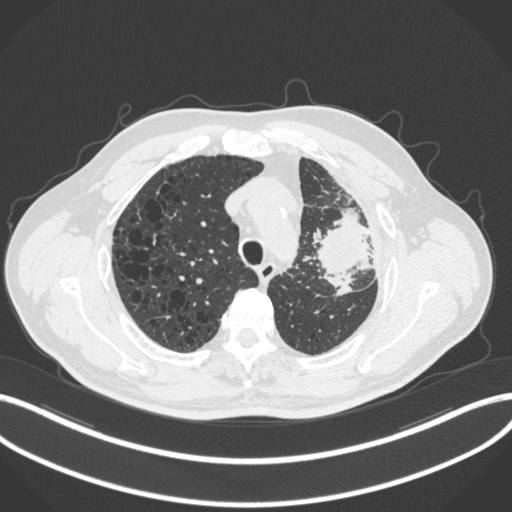
Chest CT, one axial slice. Slice 237 of 286 in the series (ordered by position). 120 kVp. Lung window (W 1500 / L -600 HU). 512 × 512 image matrix. Male patient, age 68 years. Case-level facts recorded for this patient, not image findings: clinical TNM (as recorded): T3 N3 M1.
Structures marked on this image (bounding box drawn by a radiologist):
- lung tumour (recorded histology: adenocarcinoma): box from (x=314, y=208) to (x=372, y=275) px